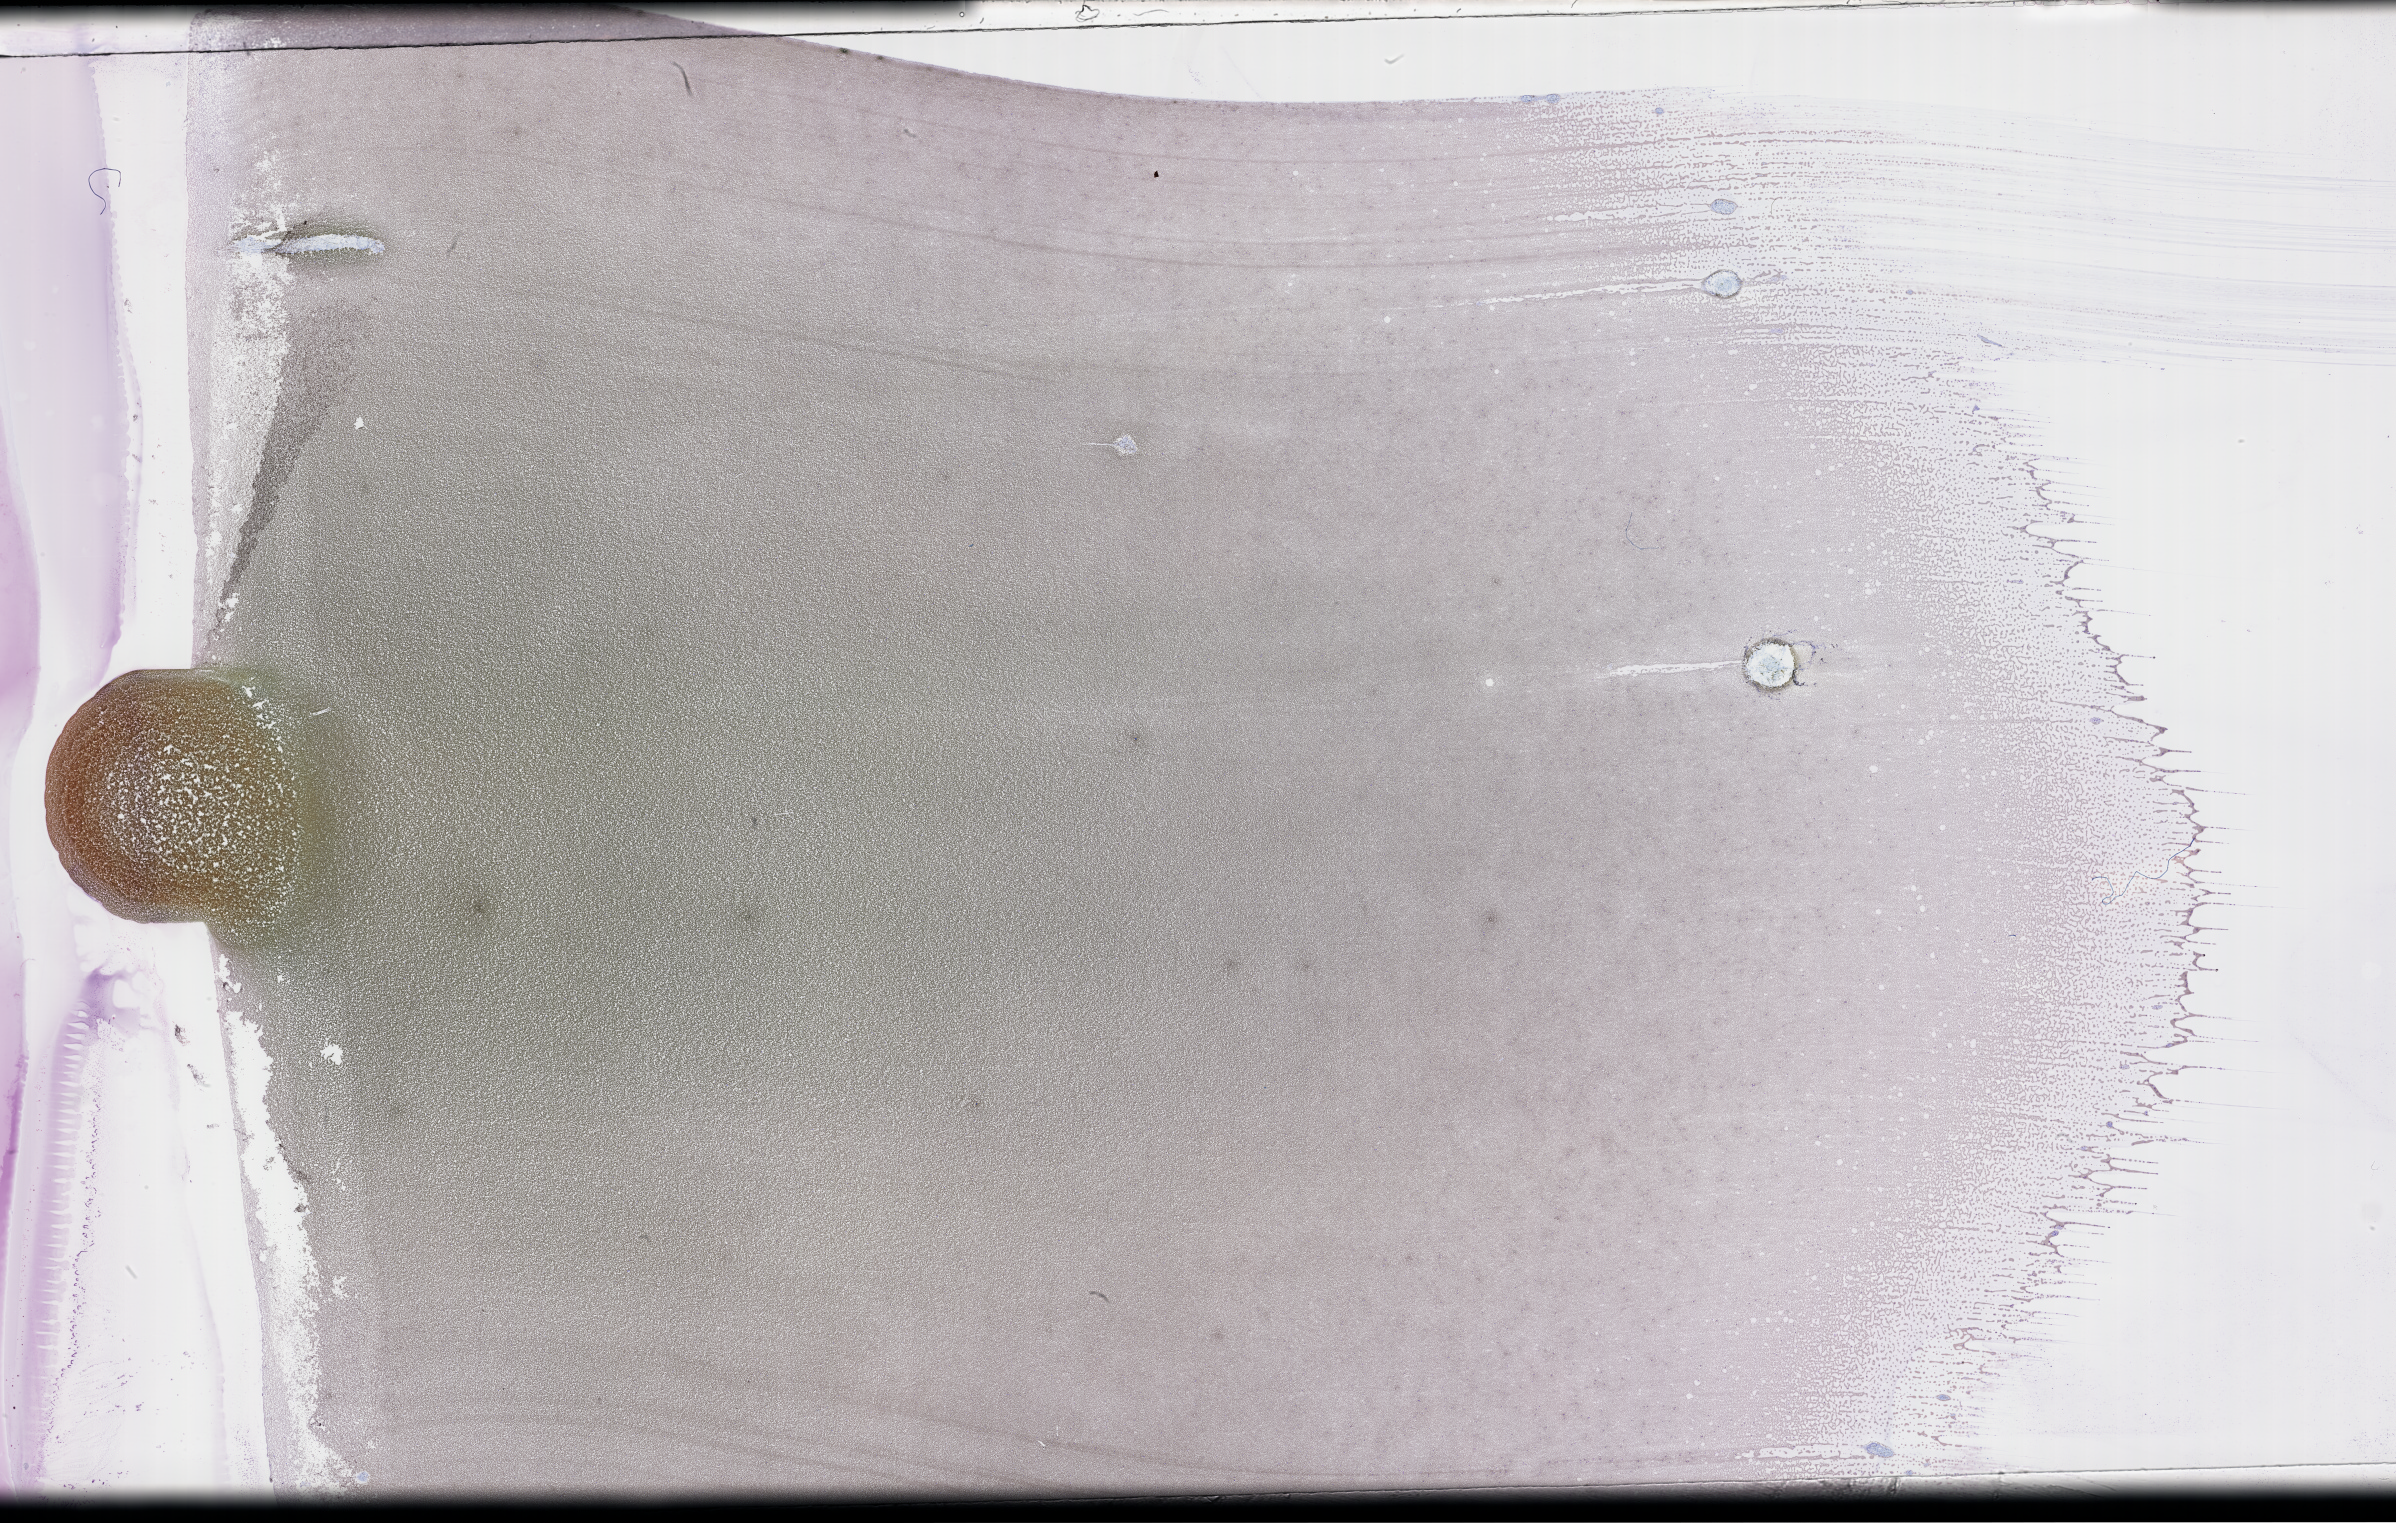
Wright–Giemsa-stained whole blood smear, whole-slide image, whole scanned area (about 38.7 x 24.6 mm) shown as a low-resolution overview. Specimen time point: collected on treatment. Patient sex: female.
Patient diagnosis: Plasma Cell Myeloma.